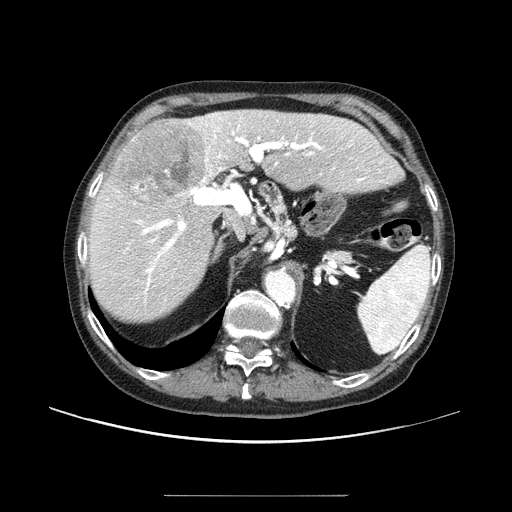
Contrast-enhanced abdominal CT (liver protocol), one axial slice; slice 59 of 91 in the series (ordered by position); reconstruction kernel STANDARD; one of 2 acquisitions stored at this slice position; soft-tissue window (W 400 / L 40 HU); 512 × 512 image matrix, field of view 400 × 400 mm. Case-level facts recorded for this patient, not image findings: diagnosis: hepatocellular carcinoma (patient treated with transarterial chemoembolisation; whether this scan precedes or follows treatment is not stated here); TNM stage (as recorded): Stage-I; Child-Pugh class: A; tumour differentiation: moderately differentiated.
Outlined on this slice (semi-automatic segmentation, software-assisted and operator-edited):
- liver parenchyma outside the tumour (the mass and vessels are separate outlines, so this box may not span the whole liver): bounding box [x1, y1, x2, y2] px = [88, 110, 400, 322]
- mass: [111, 120, 206, 206]
- liver vessels: [104, 112, 386, 304]